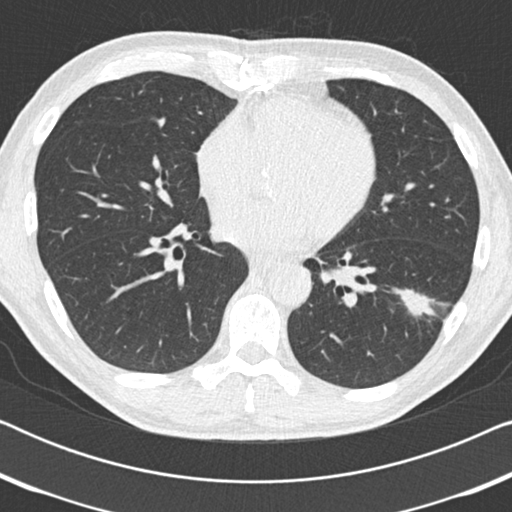
Axial slice from a low-dose chest CT screening exam; third screening round (two years after baseline); lung window (W 1500 / L -600 HU); standard (soft-tissue) reconstruction kernel (B30f); slice 106 of 186 in the series; 512 × 512 image matrix, field of view 330 × 330 mm. Male, age 59 years at enrolment. Current smoker at enrolment.
Expert-annotated lung lesion, box from (x=388, y=273) to (x=456, y=335) px. The screening reader recorded 2 non-calcified nodules or masses ≥4 mm on this exam (left lower lobe, right middle lobe); which of them this box marks is not recorded. Official screen result: positive, other. Lung cancer was diagnosed 73 days after this screen: adenocarcinoma, NOS, left lower lobe, poorly differentiated (G3), stage IA (AJCC 6th edition), 20 mm at pathology.